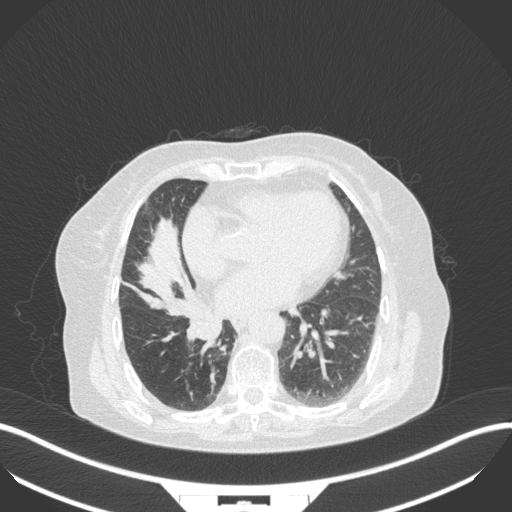
Chest CT, one axial slice. Position 126 of 329 along the scan axis. 120 kVp. Lung window (W 1500 / L -600 HU). 1 mm slice thickness. 512 × 512 image matrix. Patient: female, 75 years. Case-level facts recorded for this patient, not image findings: clinical TNM (as recorded): T1b N0 M1a; histopathological grade: G1.
Outlined on this slice (rectangle marked by the reading radiologist):
- lung tumour (recorded histology: squamous cell carcinoma): box from (x=184, y=308) to (x=228, y=349) px